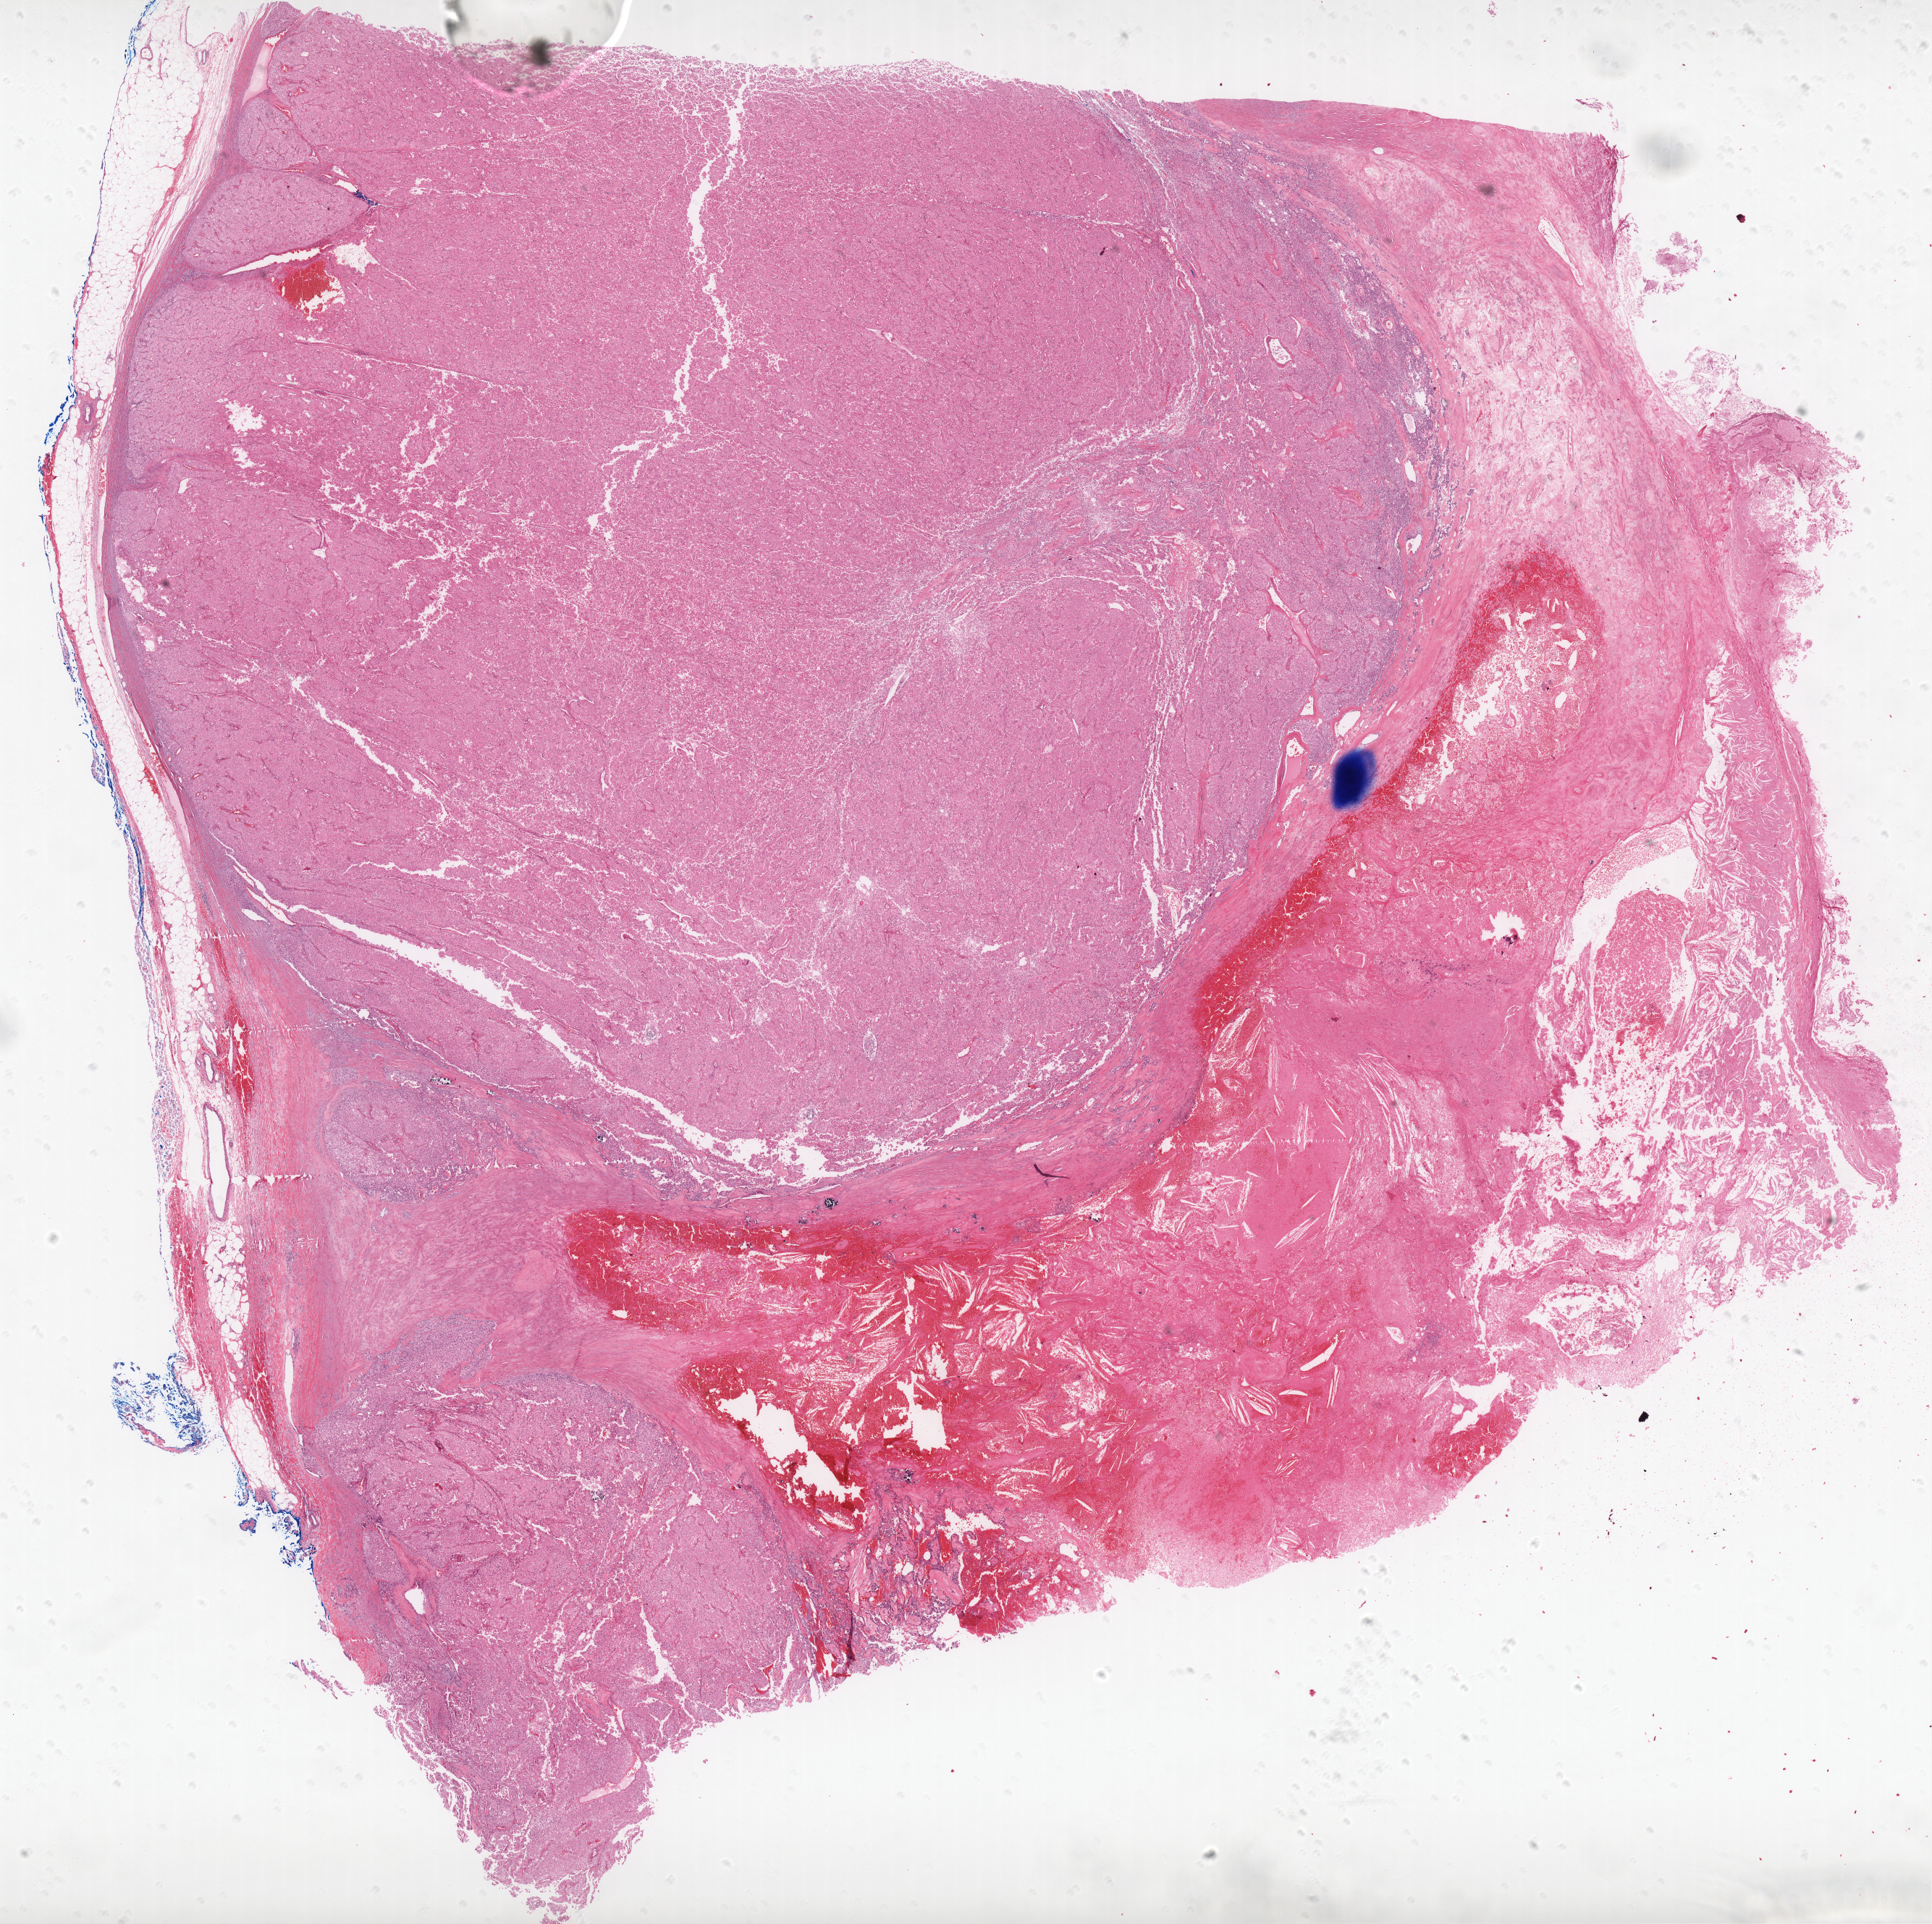
H&E whole-slide image, a low-resolution overview of the entire scanned area, about 21.3 x 21.3 mm. Formalin-fixed paraffin-embedded (FFPE) diagnostic section. Sample: primary tumour, kidney. Patient: male, age at initial diagnosis 60 years.
- pathologic diagnosis: Renal cell carcinoma, chromophobe type
- AJCC pathologic stage: II
- laterality: left
- lymph nodes positive (case pathology): 0 of 4 examined
- TNM: T2b N0 M0